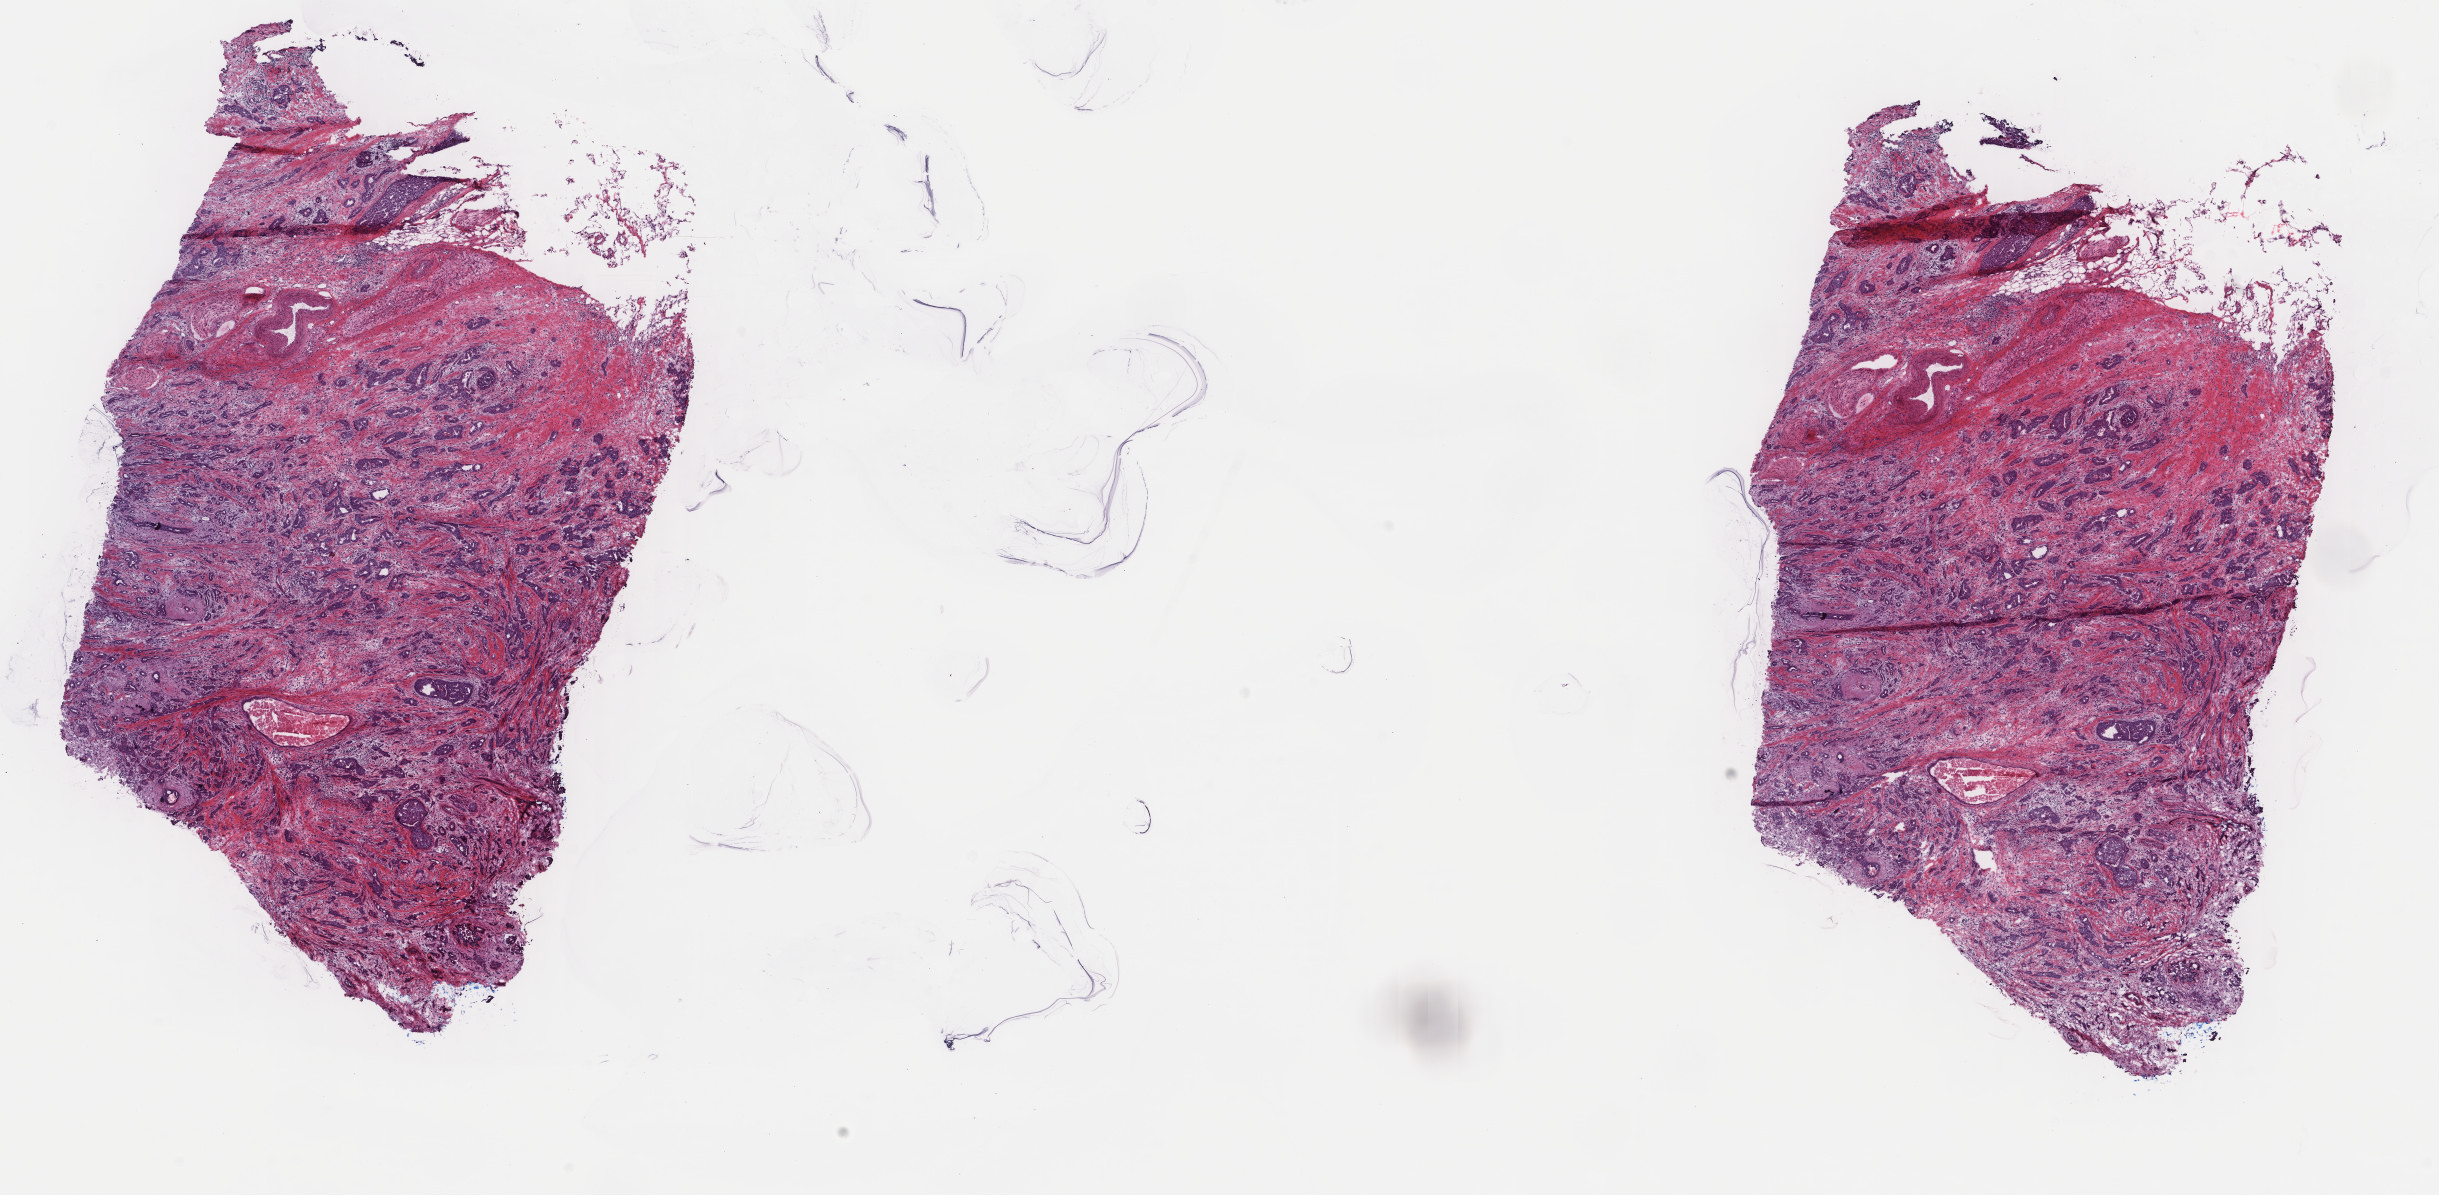
H&E whole-slide image — whole scanned area (about 19.4 x 9.5 mm) shown as a low-resolution overview, frozen section, sample: primary tumour, breast. Female, age 49 years at initial diagnosis. Pathologist review of this section (percent, as recorded): tumour cells 85%, tumour nuclei 60%, normal cells 0%, stromal cells 15%, necrosis 0%. Infiltration values recorded for this section: lymphocyte infiltration 0%, monocyte infiltration 0%, neutrophil infiltration 0%.
- TNM: T1c N2a M0
- pathologic diagnosis: Infiltrating duct carcinoma, NOS
- AJCC pathologic stage: IIIA (7th edition)